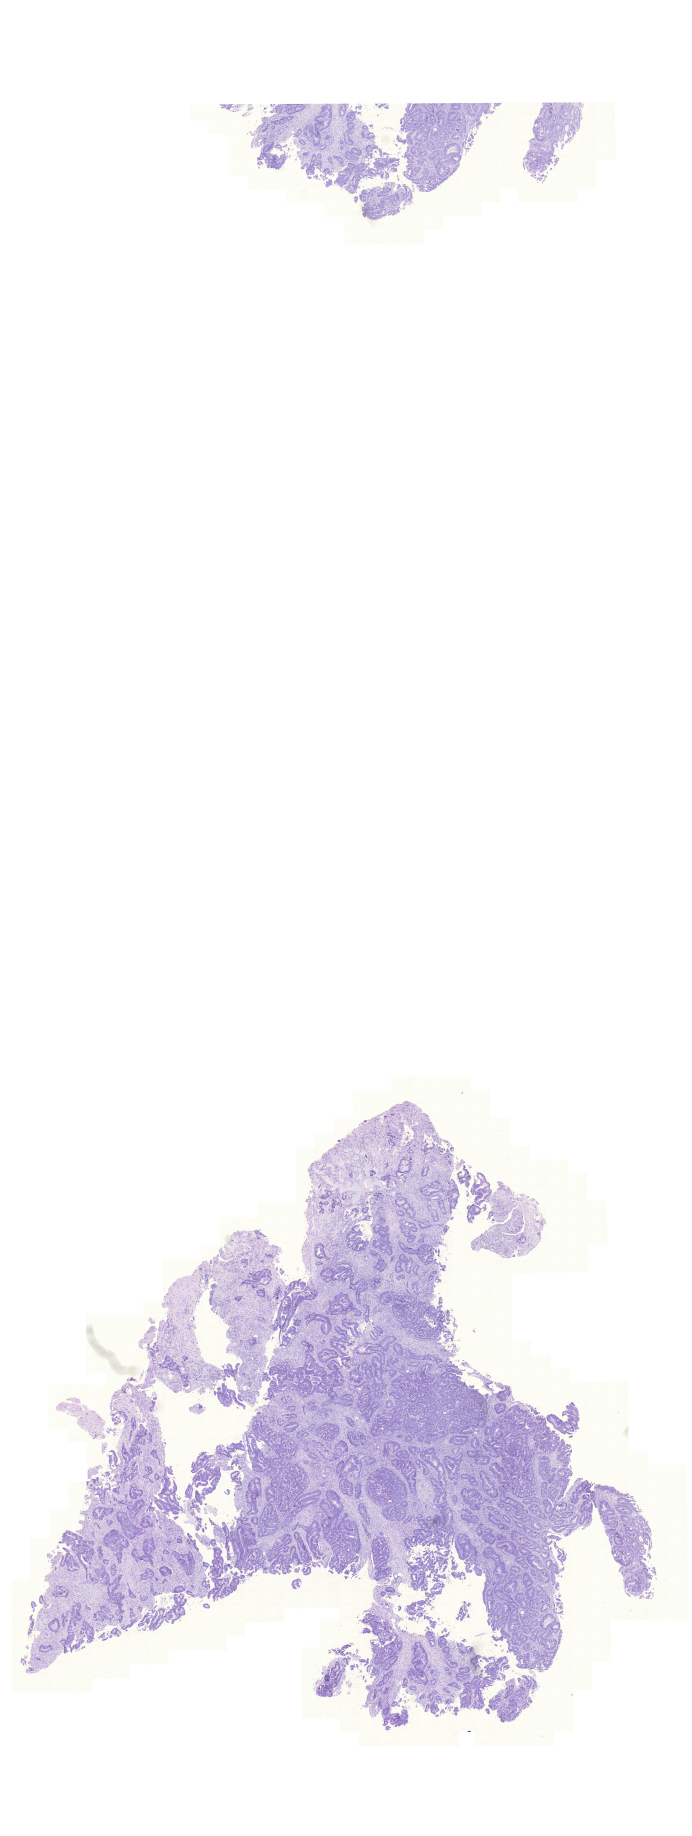
Hematoxylin and eosin (H&E) stained whole-slide image, whole scanned area (about 10.3 x 27.3 mm) shown as a low-resolution overview. Formalin-fixed paraffin-embedded (FFPE) diagnostic section. Rectum, primary tumour sample. Male patient; age at initial diagnosis 55 years.
• diagnosis: Adenocarcinoma, NOS
• AJCC pathologic stage: IV (6th edition)
• TNM: T3 N2 M1